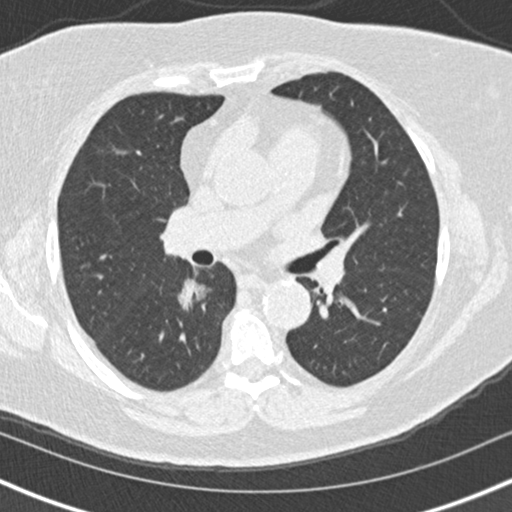
Low-dose screening chest CT, one axial slice. Reconstruction kernel B30f. Lung window (W 1500 / L -600 HU). 2 mm slice thickness. 512 × 512 image matrix, field of view 320 × 320 mm.
Annotated regions visible in this slice (outlined manually by an expert reader):
- lesion 1 (tumor, lower lobe of right lung): box from (x=178, y=278) to (x=211, y=311) px